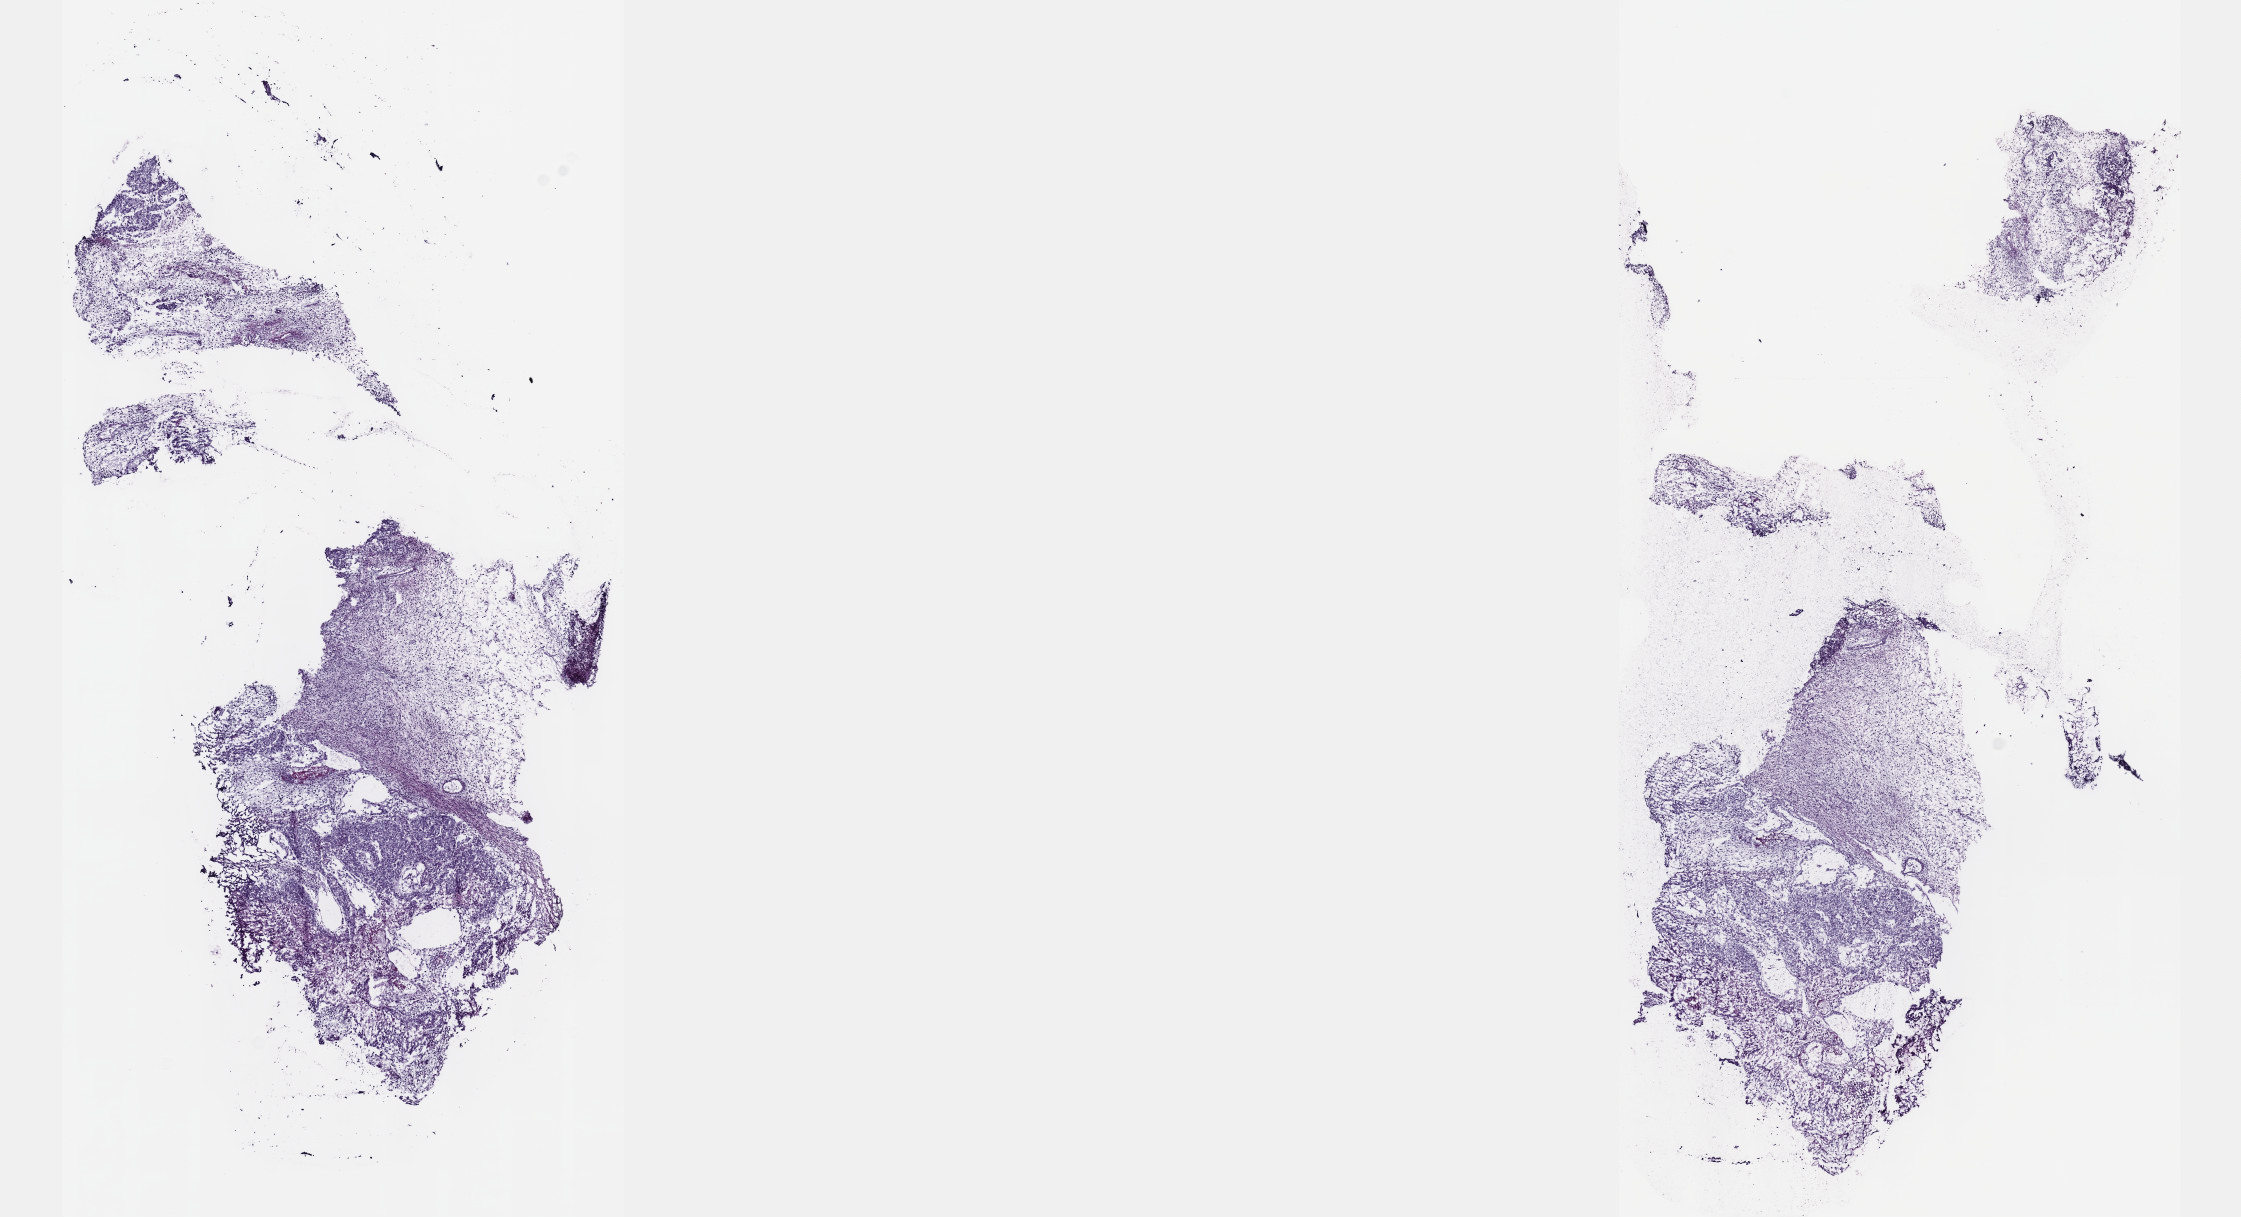
Whole-slide histology image, H&E, low-resolution overview of the scanned area, about 18.1 x 9.8 mm (slide scanned at 40x). Frozen section from the top of the tissue portion. Primary tumour sample from the testis. Male, age 39 years at initial diagnosis. Slide review estimates, as recorded: tumour cells 80%, tumour nuclei 80%, normal cells 0%, stromal cells 10%, necrosis 10%. Infiltration values recorded for this section: lymphocyte infiltration 60%, monocyte infiltration 10%, neutrophil infiltration 20%.
Laterality: right. AJCC pathologic stage: IIIB (5th edition). Pathologic diagnosis: Mixed germ cell tumor.